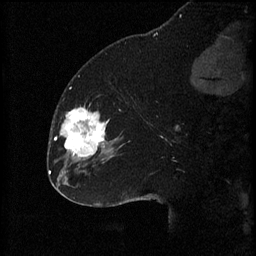
Breast MRI (dynamic contrast-enhanced), one sagittal slice; position 24 of 60 along the scan axis; 3 images stored at this slice position (order not interpretable as contrast timing); 1.5 T; TE 4.2 ms, TR 8.2 ms; 2 mm slice thickness; 256 × 256 image matrix, field of view 180 × 180 mm. Patient: female, 32 years.
Structures marked on this image (semi-automatically segmented with operator editing):
- analysis volume of interest (the breast-tissue region the enhancement analysis was run in; not a lesion): bounding box [x1, y1, x2, y2] px = [58, 106, 111, 165]
- tumour enhancement mask (voxels above the 70 % enhancement threshold inside the analysis volume of interest): [60, 108, 106, 159]